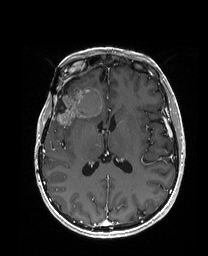
Brain MRI from a brain-tumour surgery series, one axial slice. Slice 86 of 192 in the series (ordered by position). T1-weighted post-contrast. 1 mm slice thickness. 208 × 256 image matrix, field of view 203 × 250 mm. From the clinical record (not read from this slice): histopathology: Metastatic Carcinoma from Breast primary.
Structures marked on this image (manually delineated by an expert):
- previous resection cavity: bounding box <56,81,72,114> (left, top, right, bottom; pixels)
- tumour: <55,86,104,126>